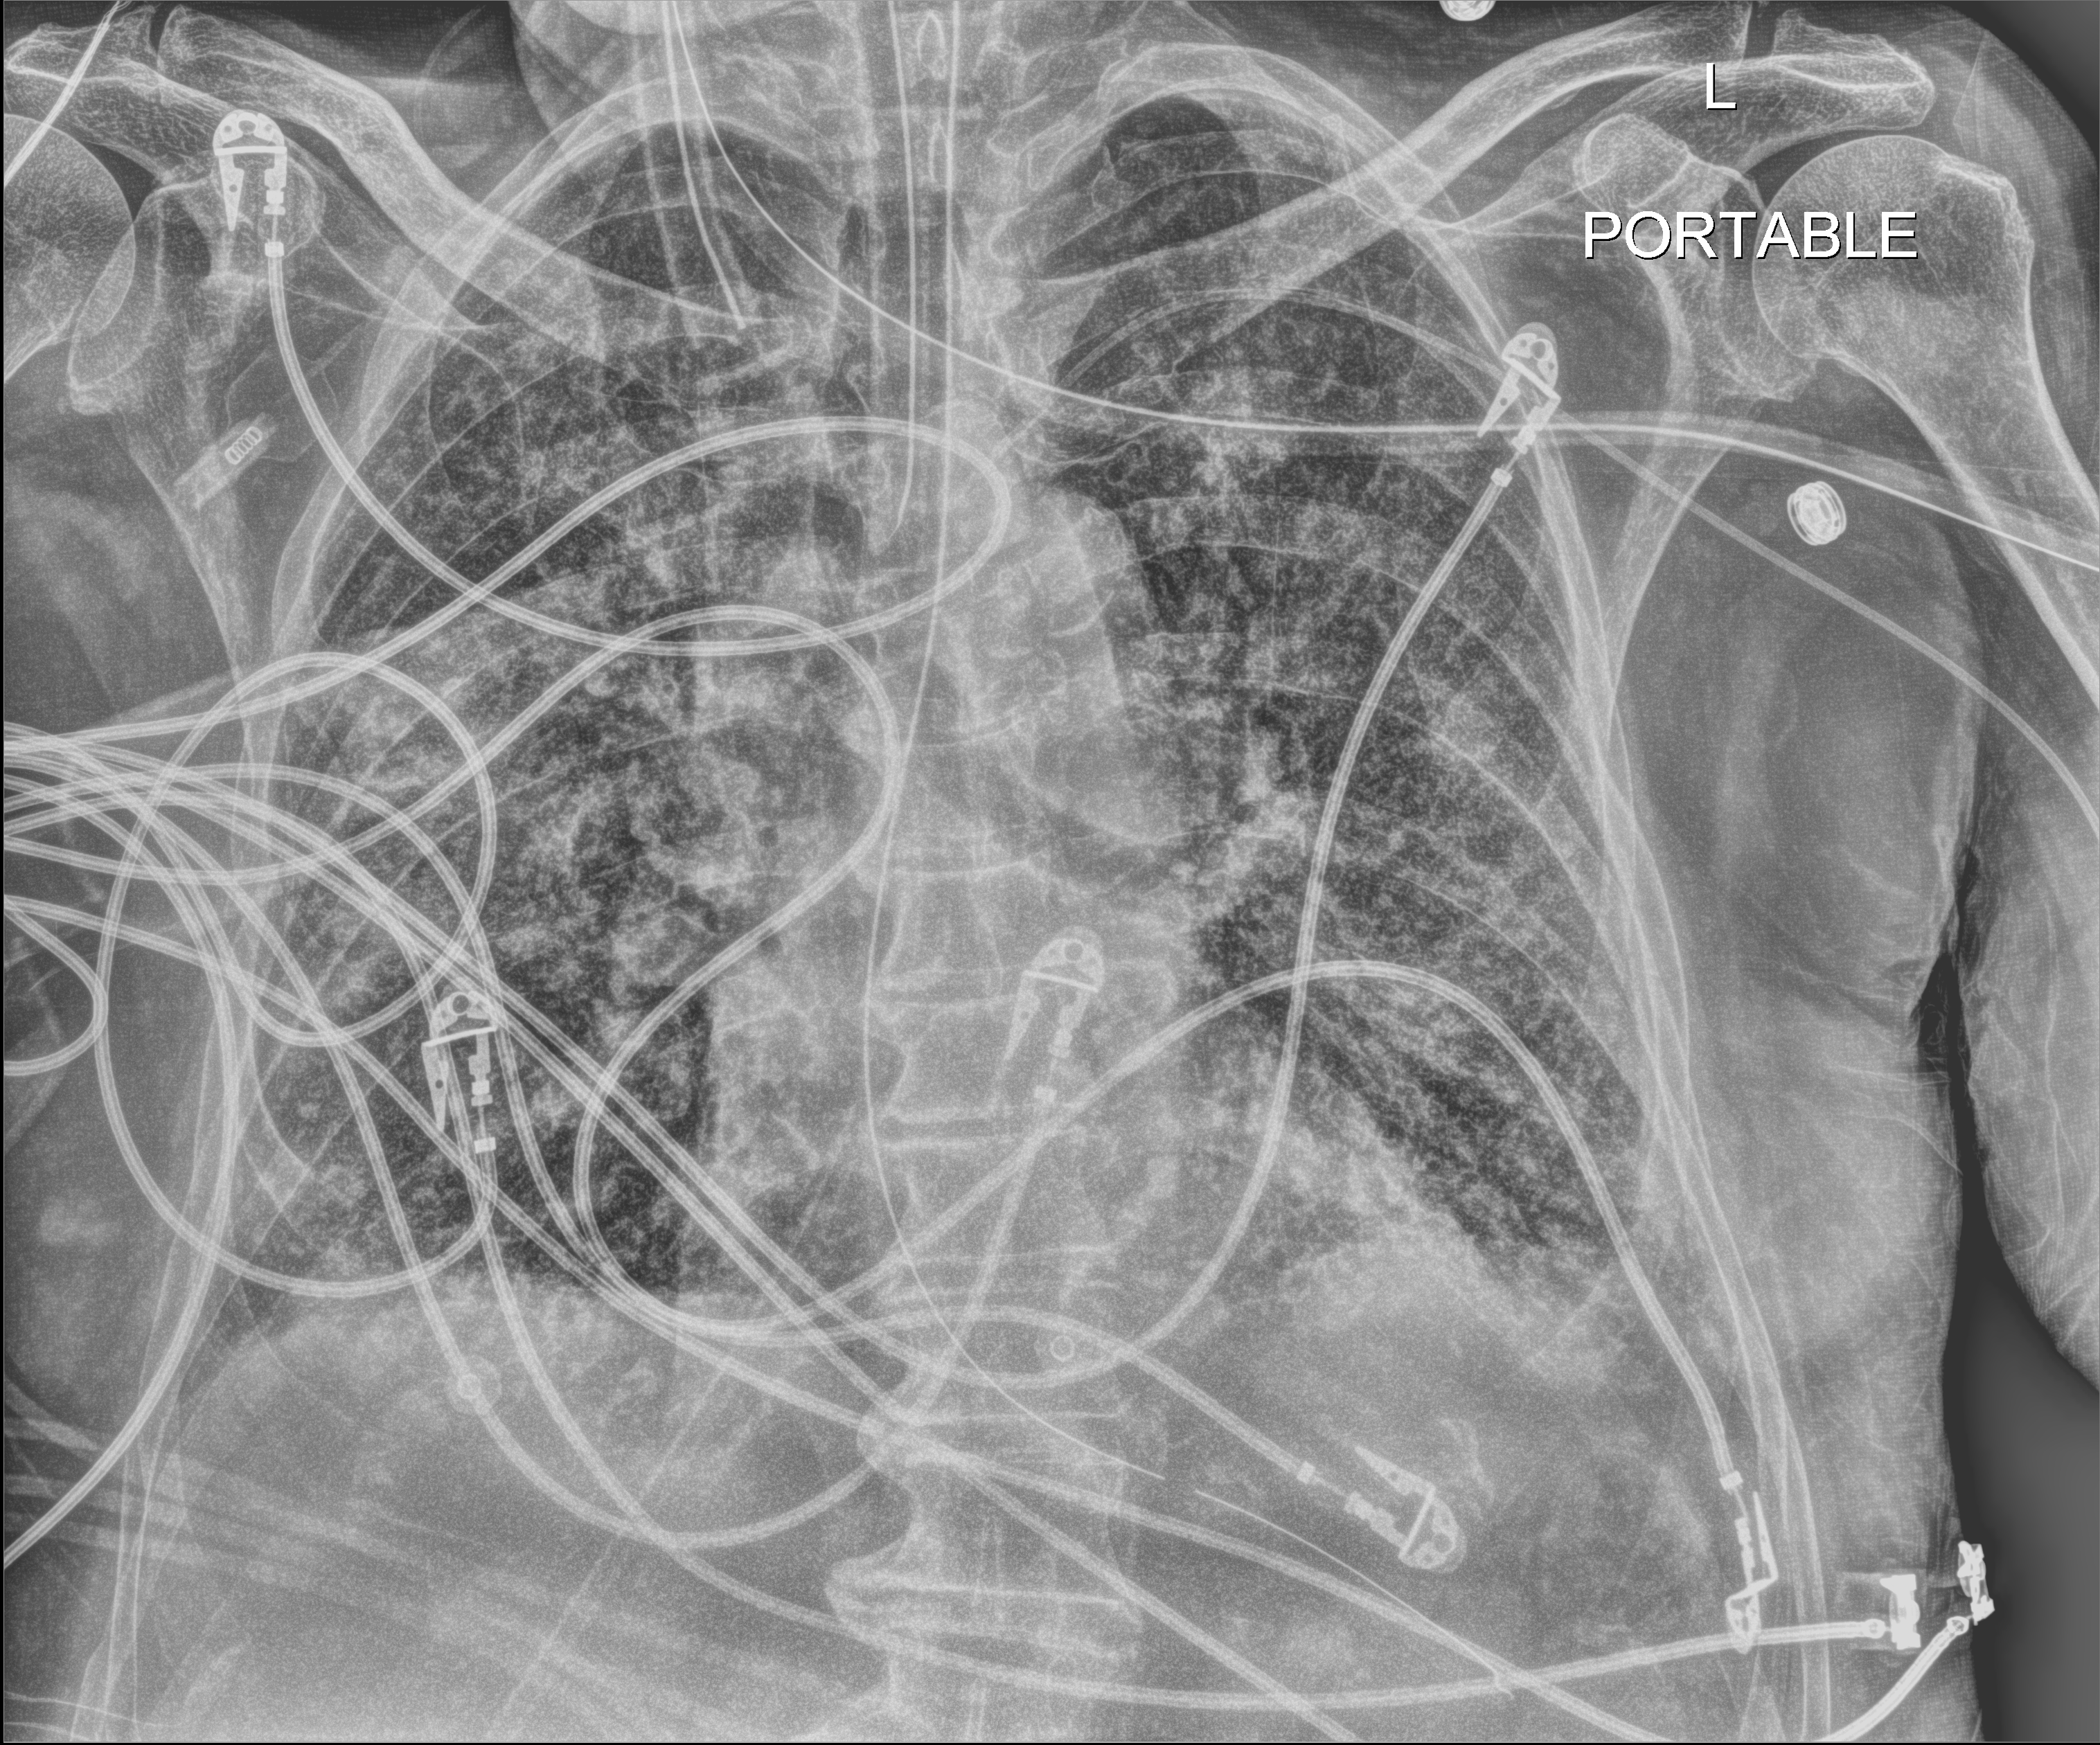
Portable chest radiograph, anteroposterior (AP) projection. Patient hospitalised with COVID-19; male, aged 75–90 years.
From the hospital-stay record, not from the radiograph (when in the stay this image was taken is not recorded): mechanically ventilated during this hospital stay: yes.